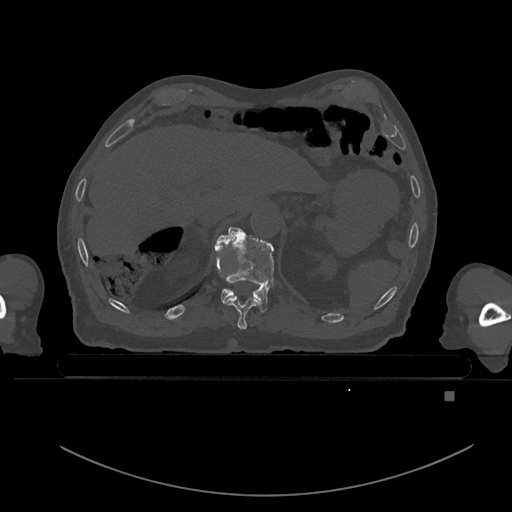
CT including the spine, one axial slice. Slice 56 of 969 in the series (ordered by position). Bone window (W 1800 / L 400 HU). 512 × 512 image matrix, field of view 456 × 456 mm. Patient: male, 82 years. From the clinical record (not read from this slice): primary cancer: prostate; vertebrae with lytic lesions (as recorded): T11, T9, T8, T2.
Structures marked on this image (semi-automatic segmentation, software-assisted and operator-edited):
- T10 vertebra: box from (x=225, y=296) to (x=260, y=330) px
- T11 vertebra: (x=217, y=226)–(x=274, y=313)